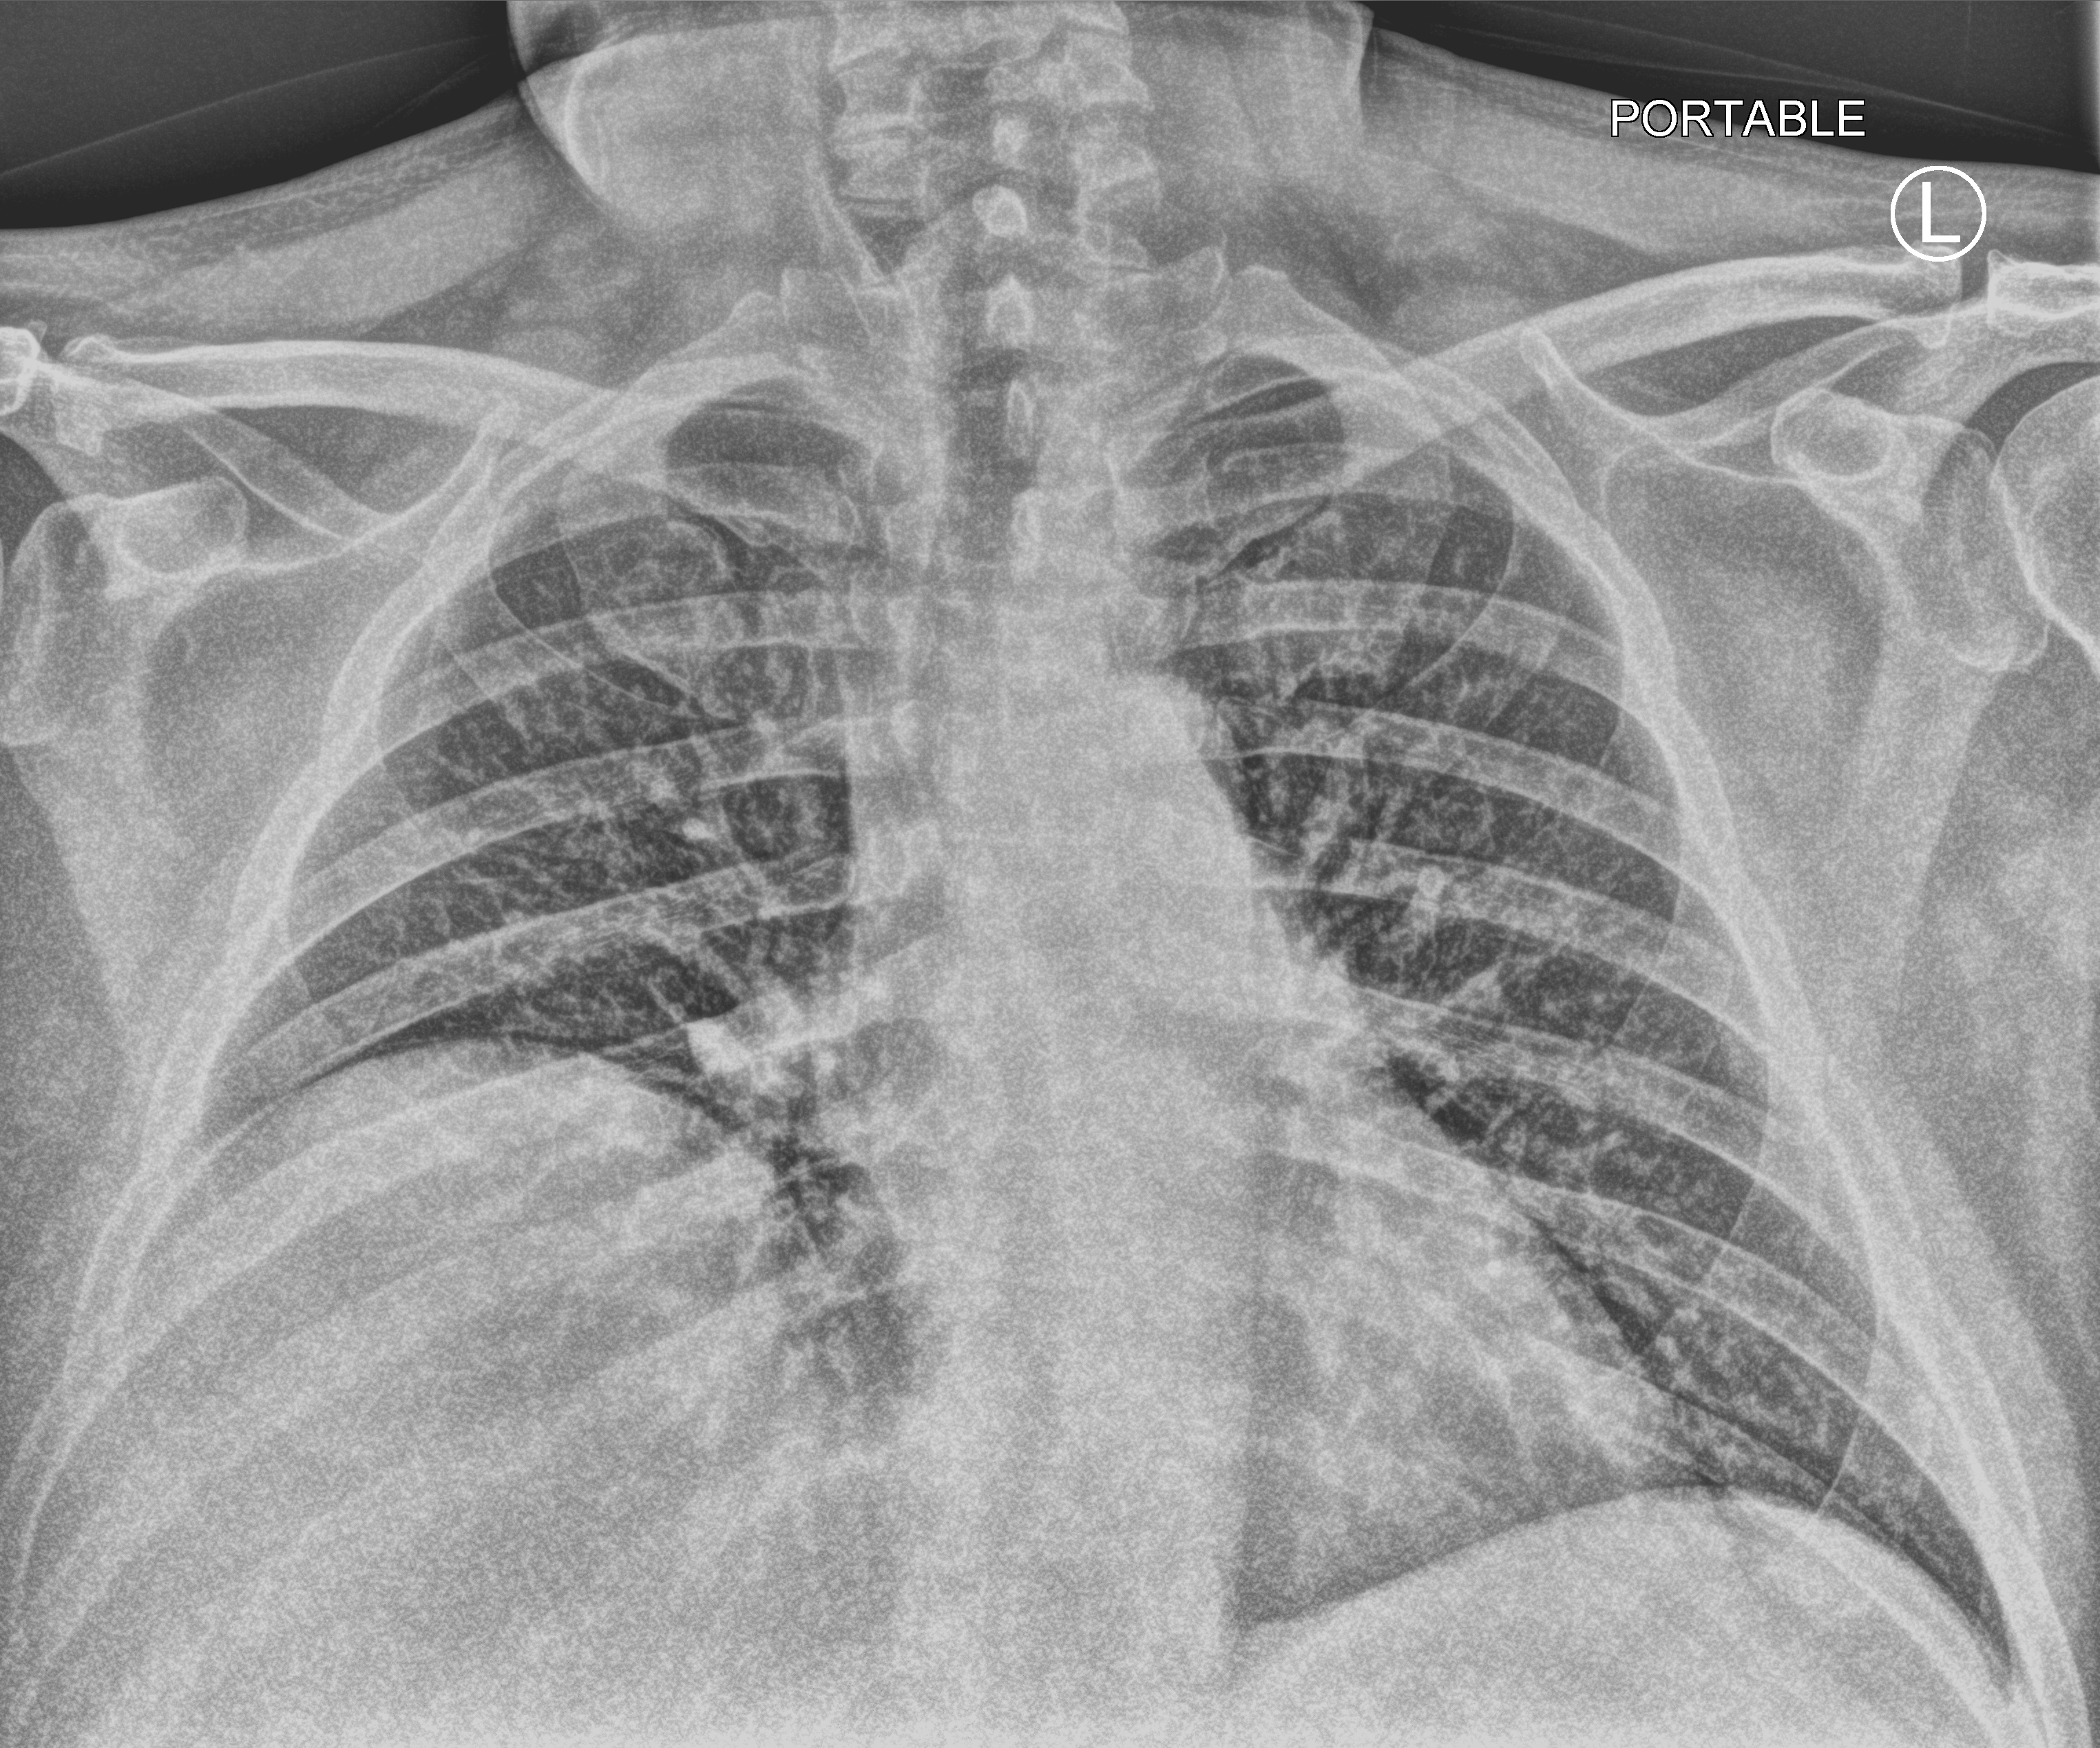
Bedside chest radiograph (computed radiography). Male patient hospitalised with COVID-19, age 18–59 years.
From the hospital-stay record, not from the radiograph (when in the stay this image was taken is not recorded): mechanically ventilated during this hospital stay: yes.